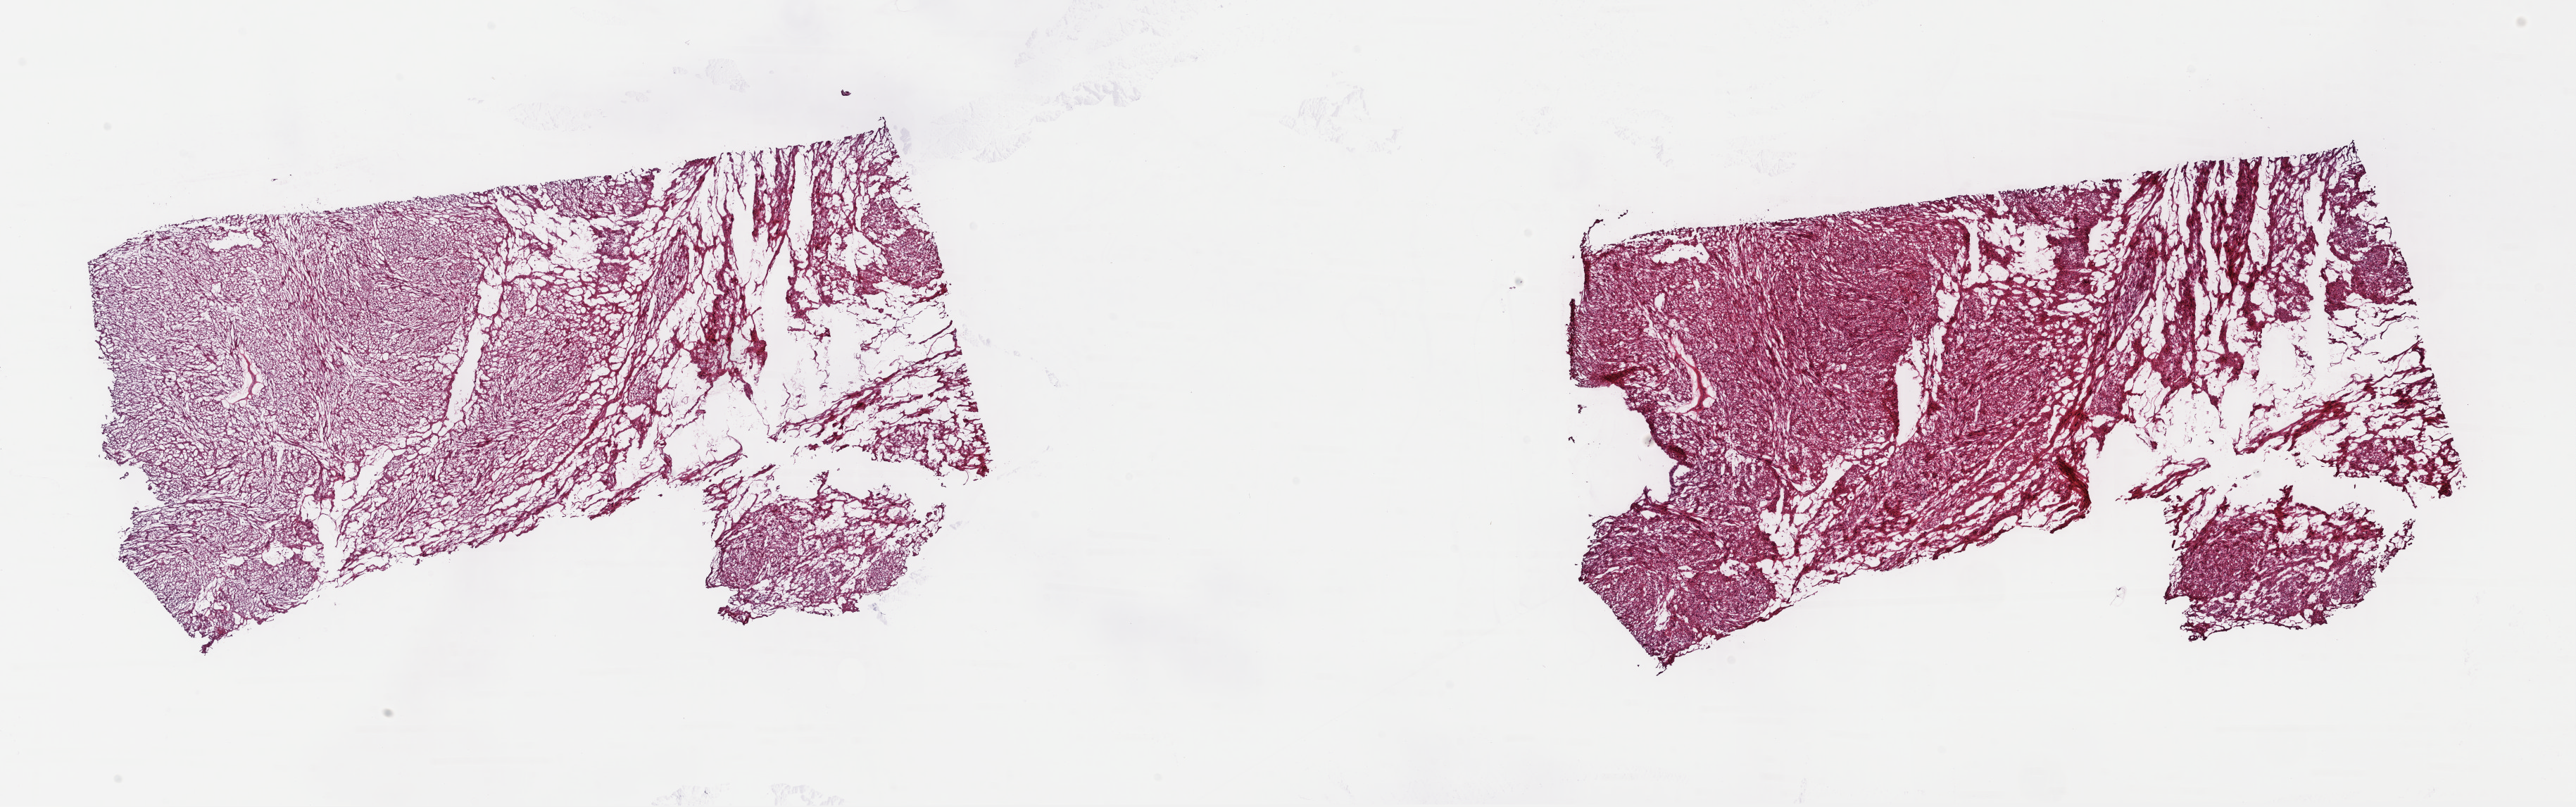
Digitized H&E tissue section (whole slide), a low-resolution overview of the entire scanned area, about 28.8 x 9.0 mm (acquisition: 40x scan). Frozen section. Primary tumour sample from the retroperitoneum and peritoneum. Patient: male, age at initial diagnosis 67 years. Slide review estimates, as recorded: tumour cells 85%, tumour nuclei 100%, normal cells 0%, stromal cells 15%, necrosis 0%. Infiltration values recorded for this section: lymphocyte infiltration 0%, monocyte infiltration 0%, neutrophil infiltration 0%.
Histologic diagnosis: Leiomyosarcoma, NOS (retroperitoneum).